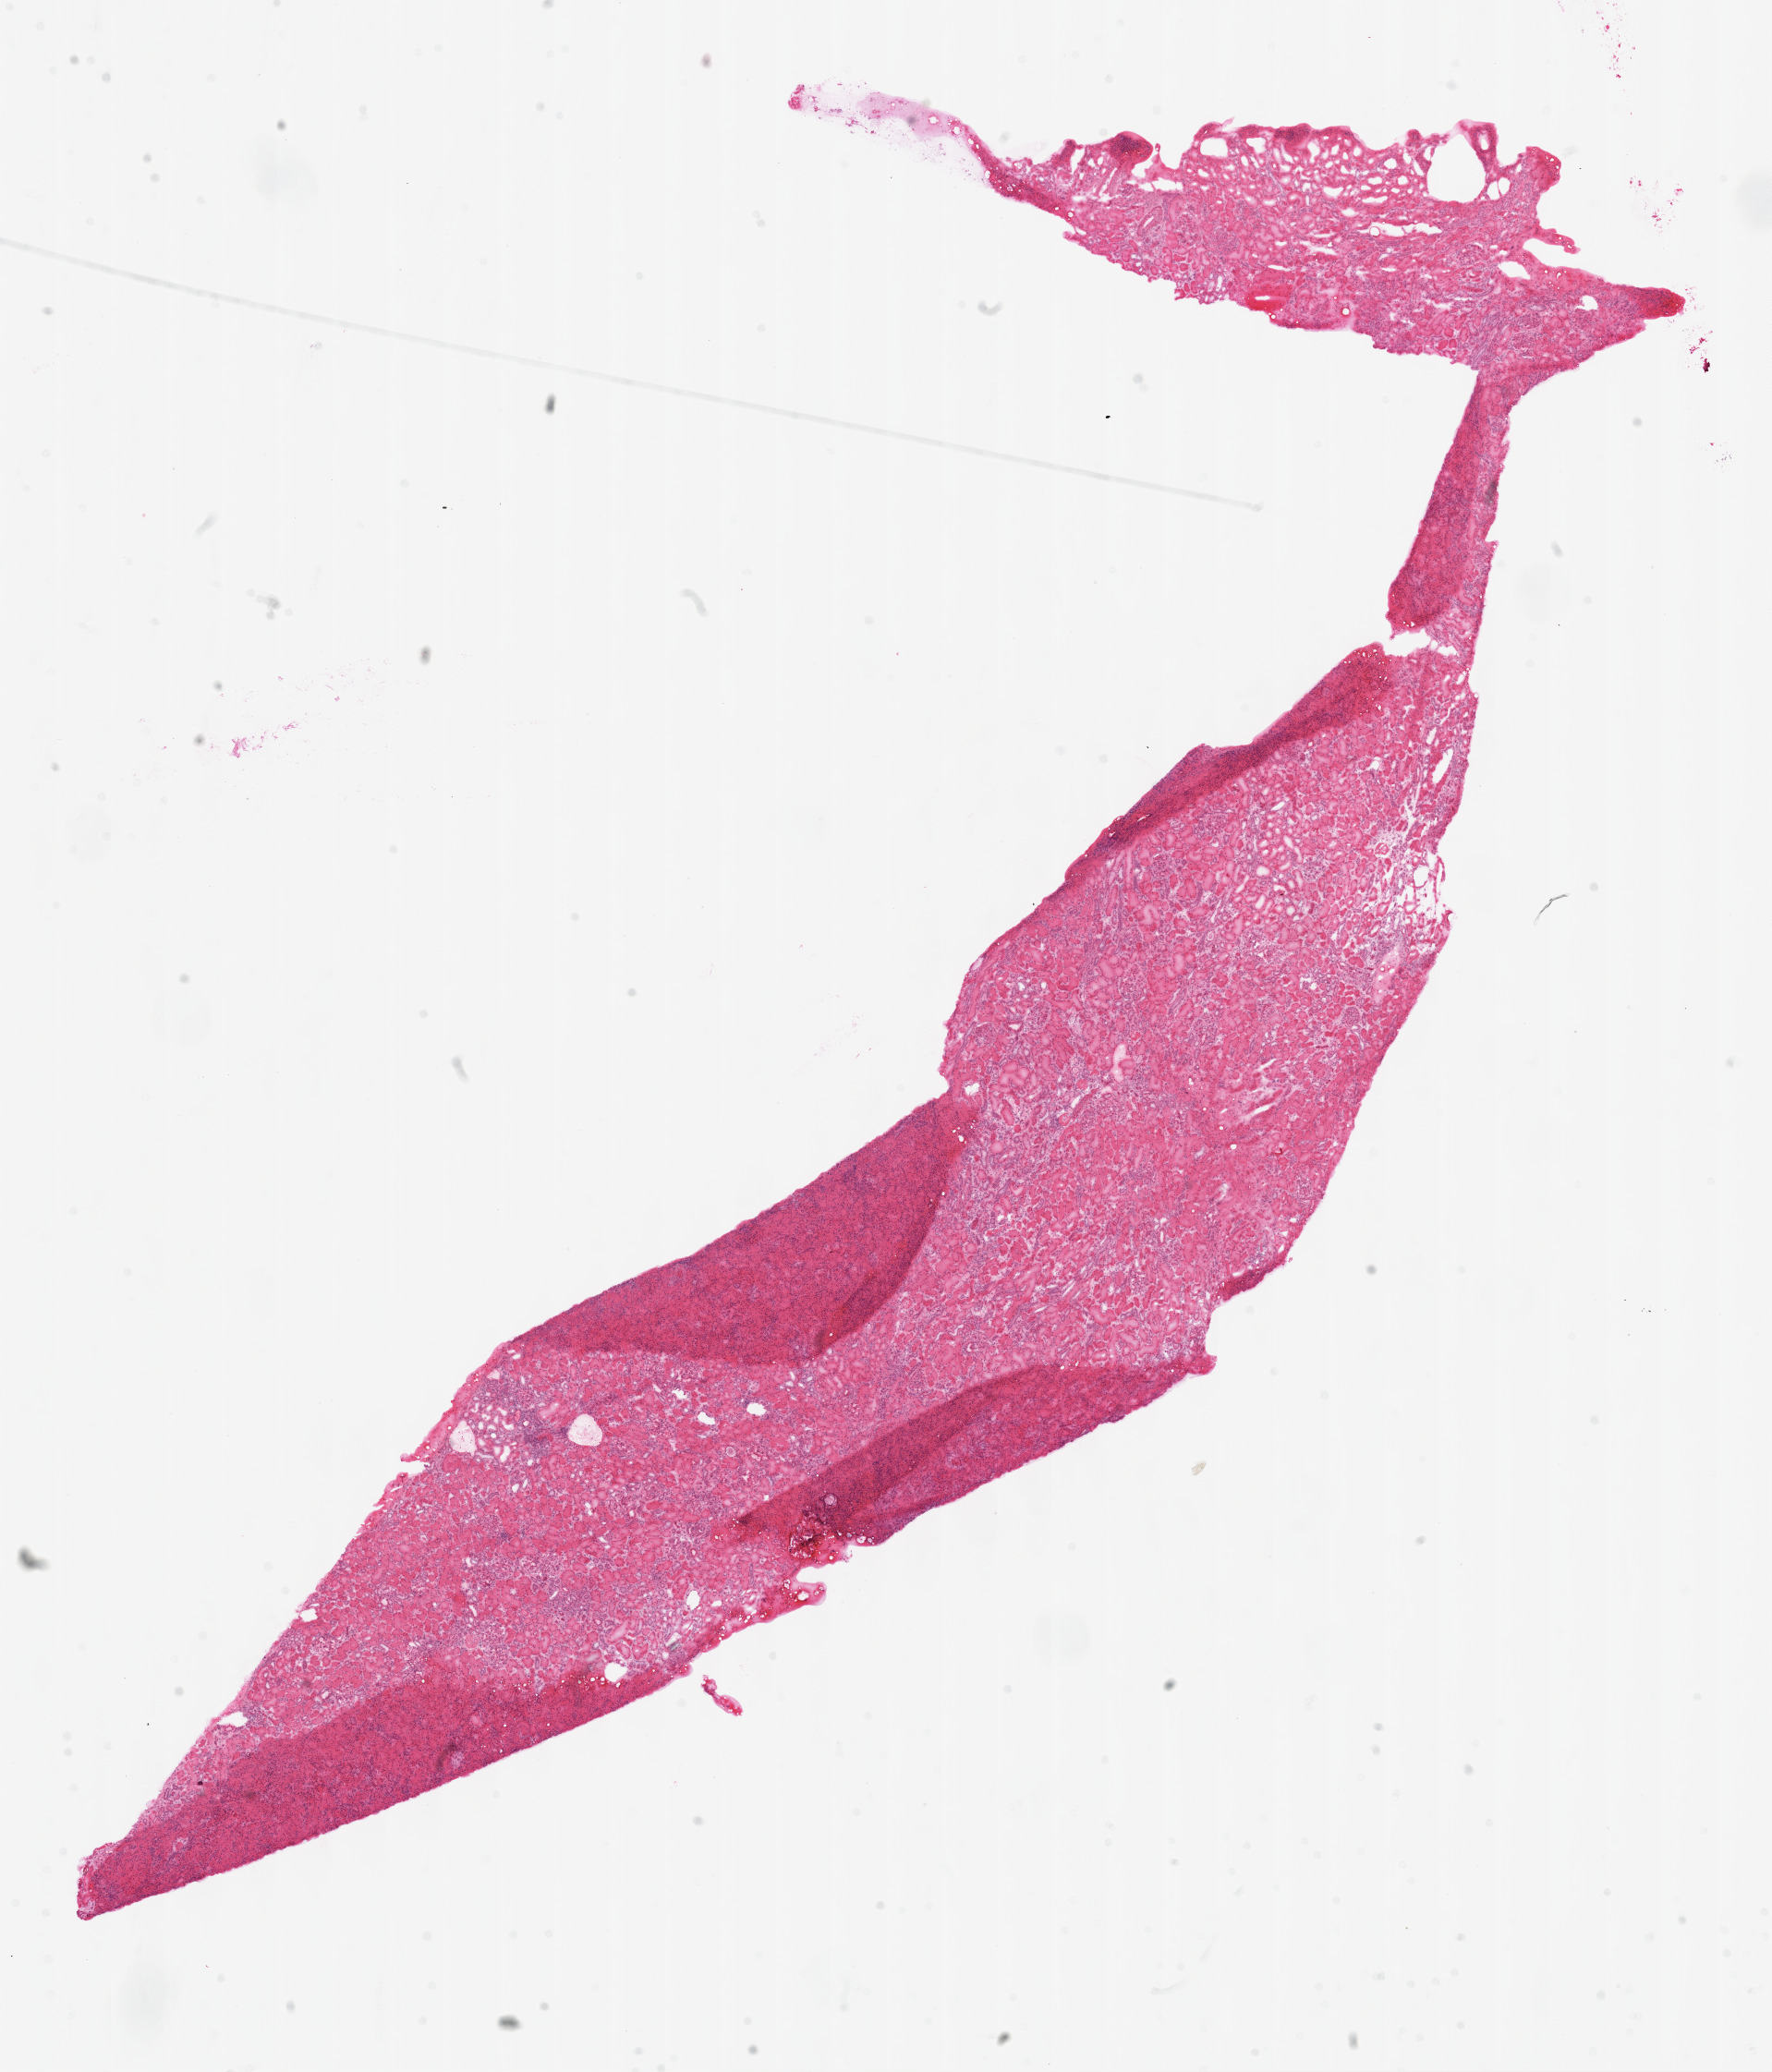
H&E-stained whole-slide image — whole scanned area (about 15.5 x 18.1 mm, from a 20x scan) shown as a low-resolution overview; frozen section; solid tissue normal (non-tumour tissue) sample from the kidney. Female, age 54 years at initial diagnosis.
* this section: solid tissue normal (non-tumour) sample from the same patient
* patient diagnosis: Clear cell adenocarcinoma, NOS